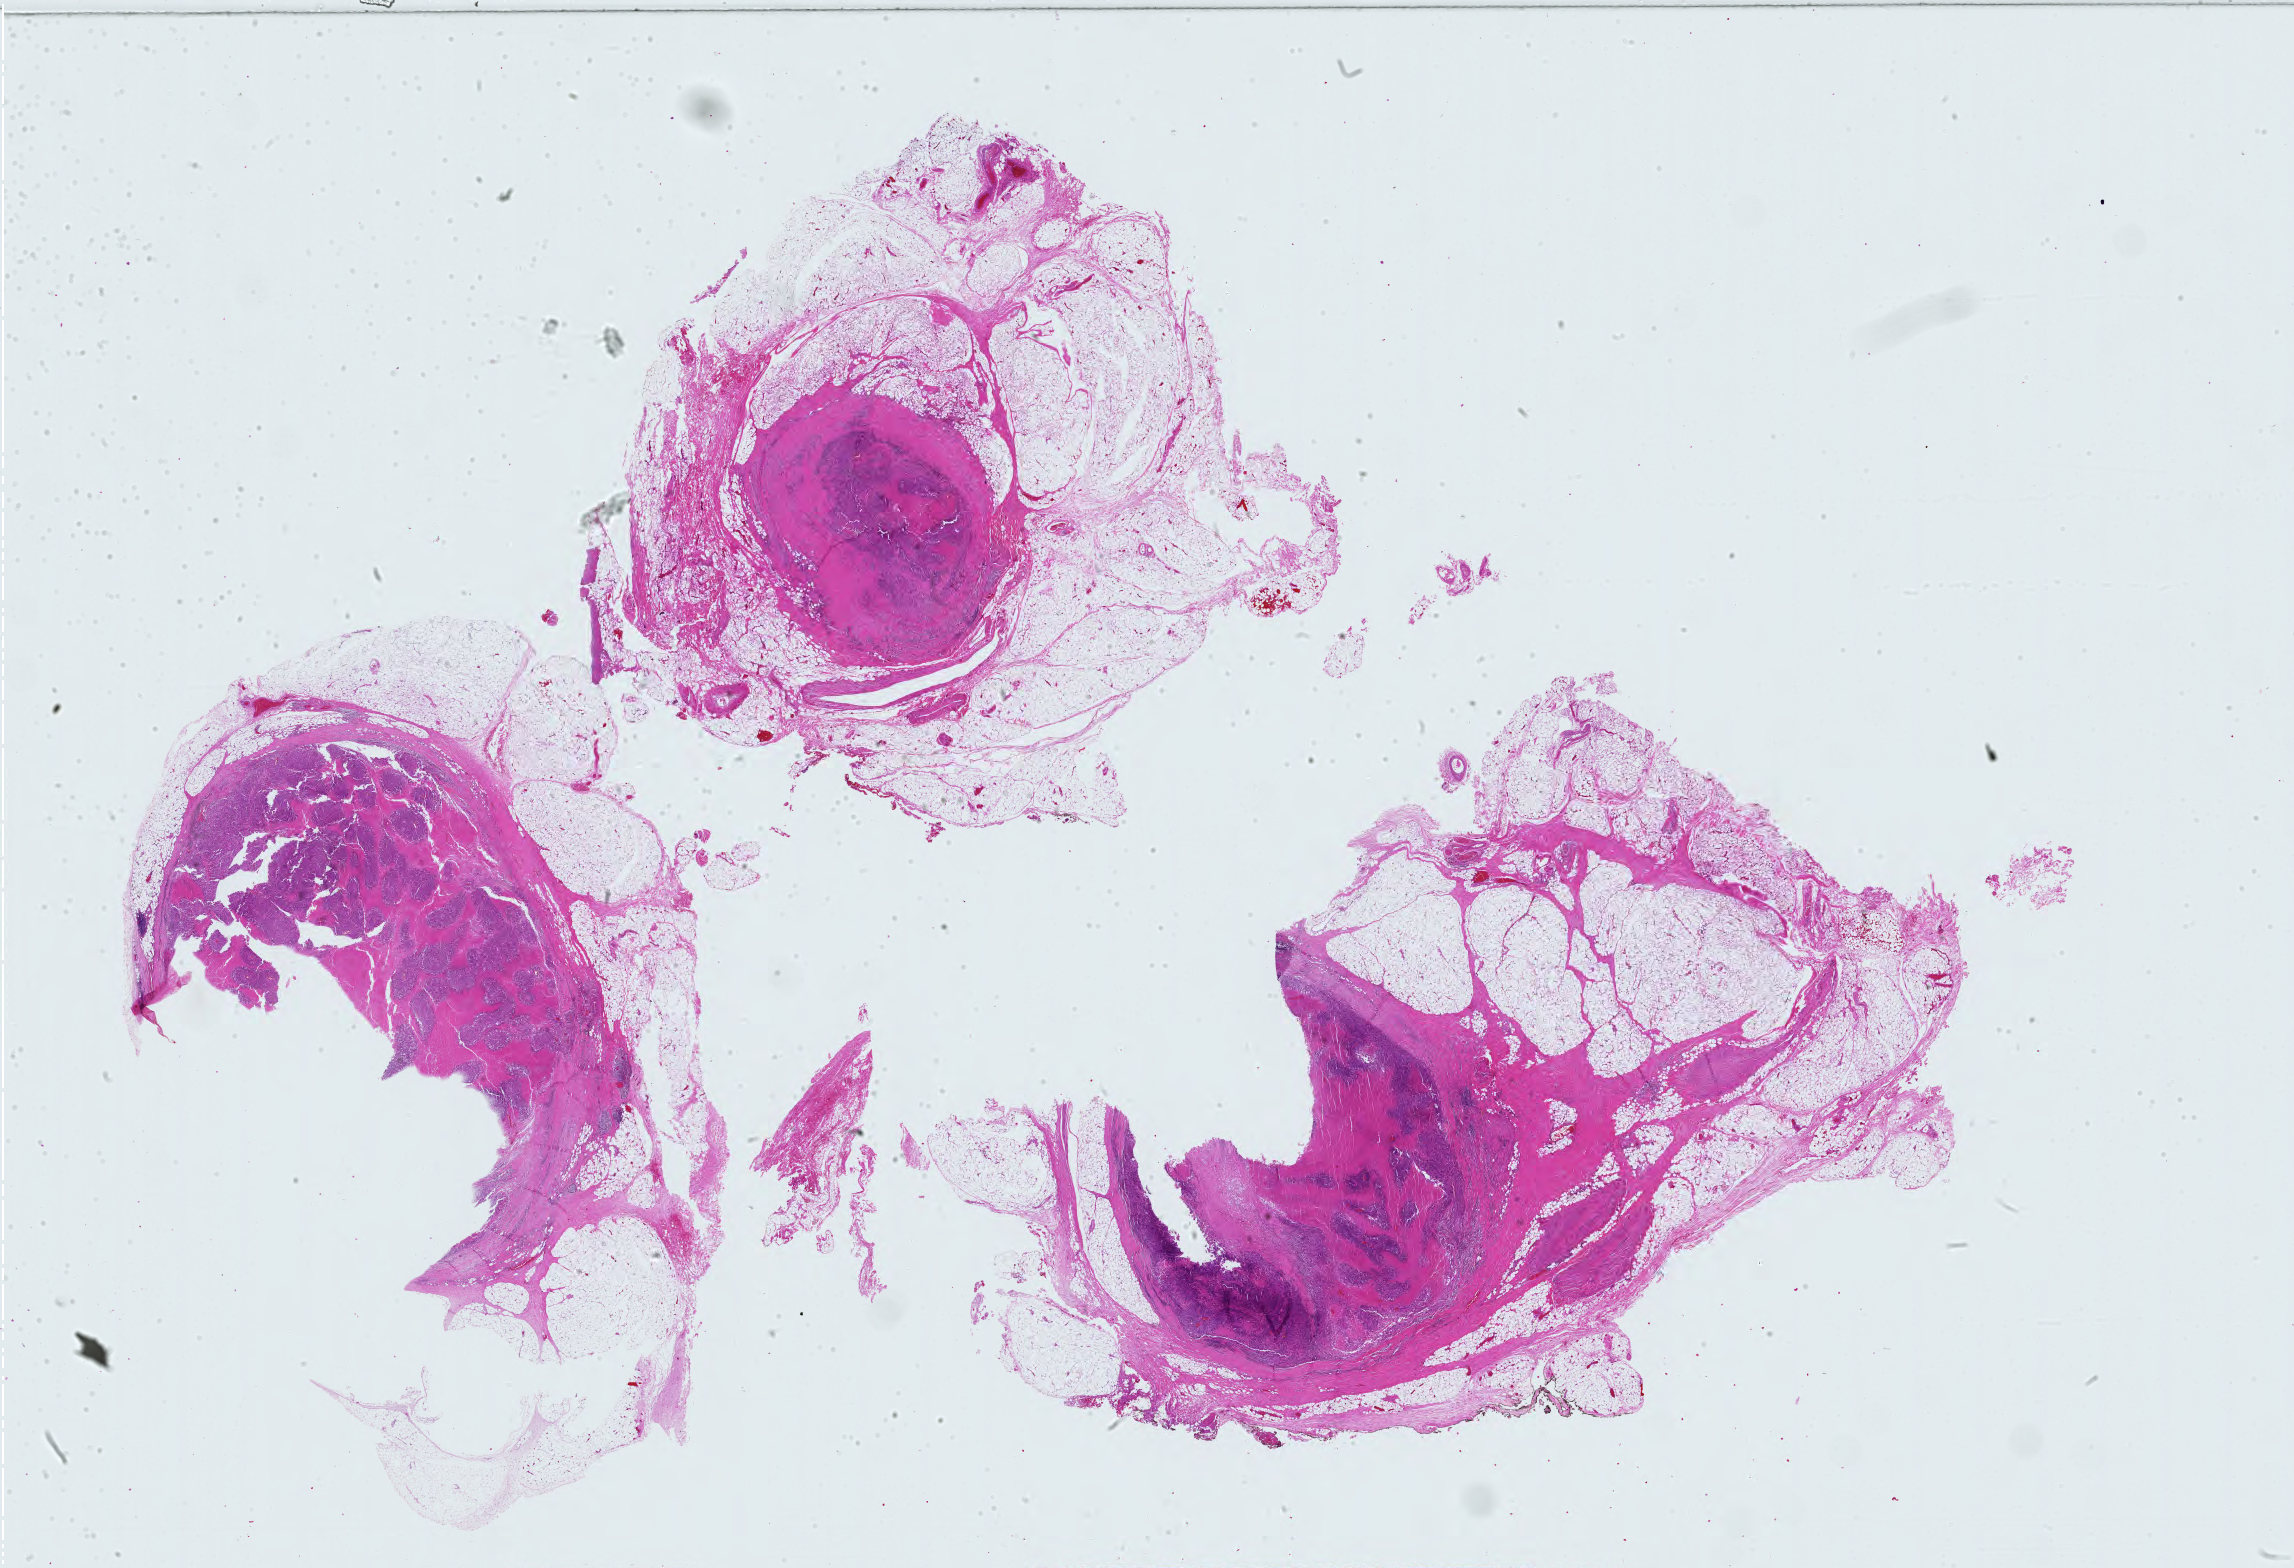
Whole-slide histology image, Hematoxylin and eosin (H&E) stained, a low-resolution overview of the entire scanned area, about 33.3 x 22.7 mm. Formalin-fixed paraffin-embedded (FFPE) diagnostic section. Primary tumour sample from the skin. Male, age 73 years at initial diagnosis.
Histologic diagnosis: Malignant melanoma, NOS. AJCC pathologic stage: IIIC (7th edition).